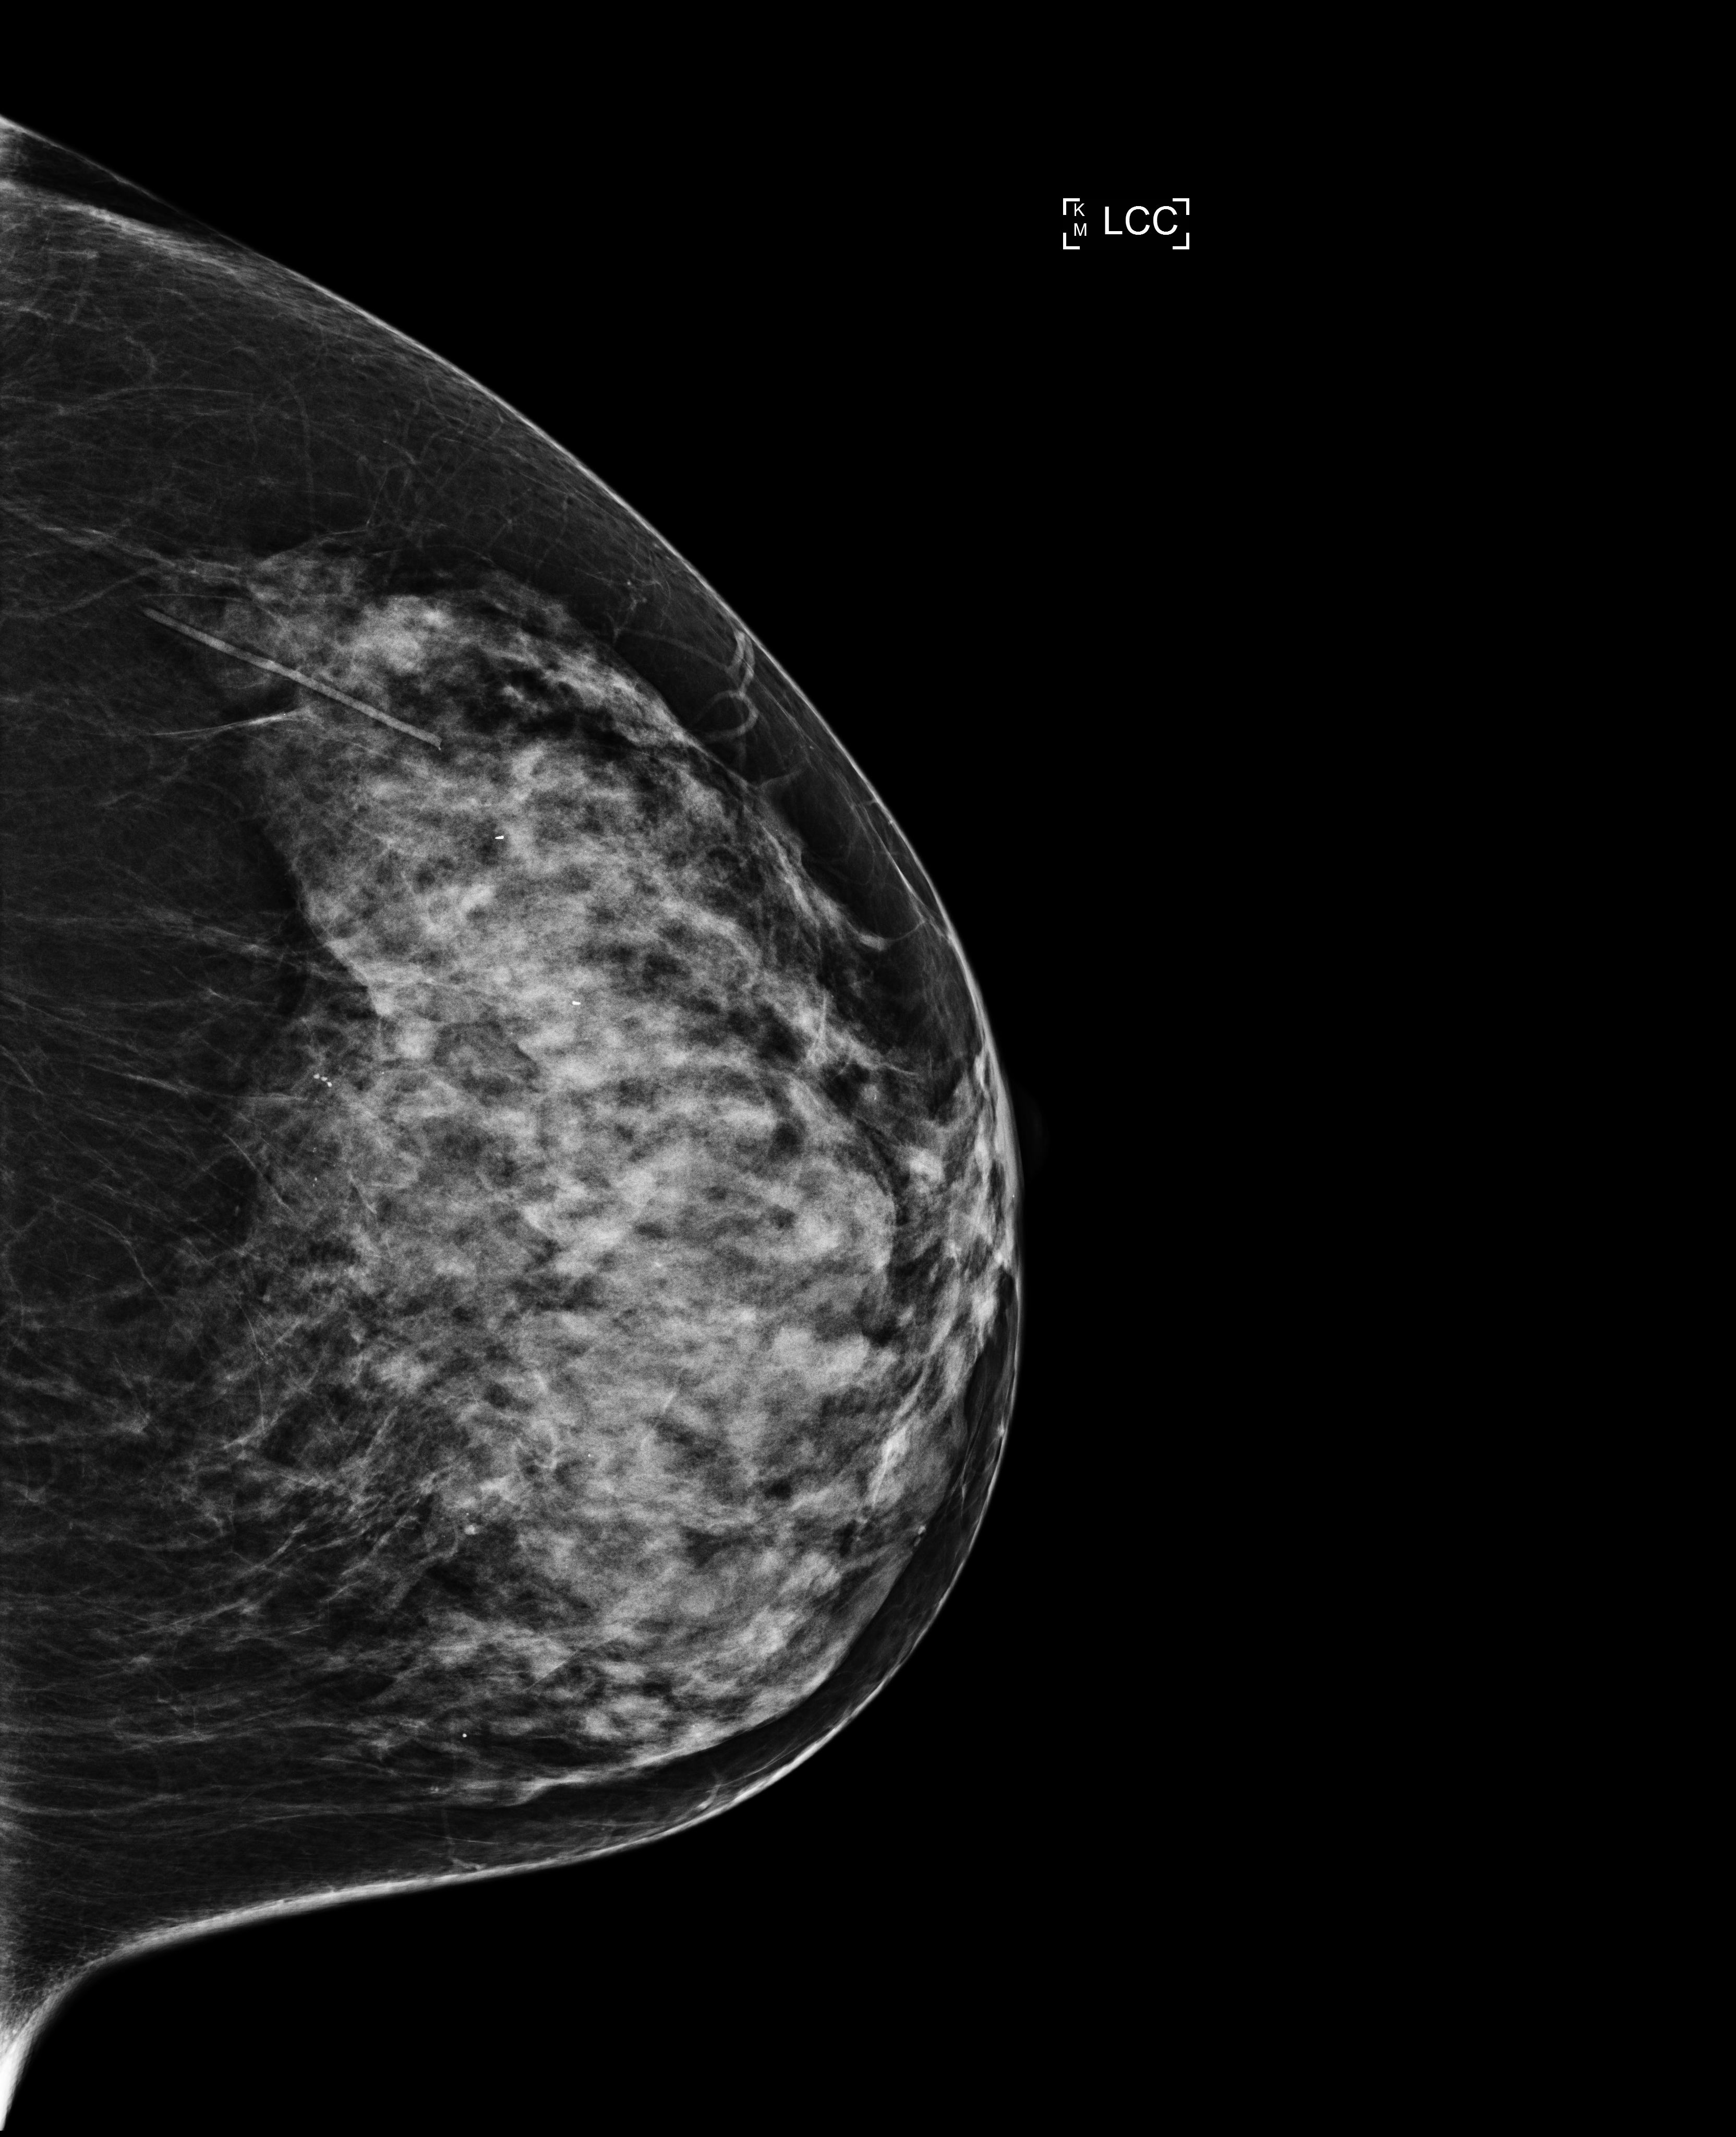
Screening examination; compressed breast thickness 56 mm. Patient aged 56 years (female).
Image type: full-field digital mammogram. Breast: left. Projection: CC view. Breast density at the screening exam (both breasts): extremely dense (BI-RADS density category d). Final BI-RADS category for the screening round (tomosynthesis exam, both breasts): category 2. Recall: no recall after this screen.